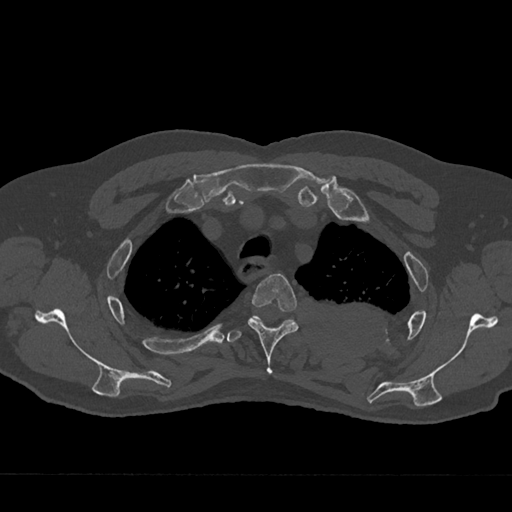
CT including the spine, one axial slice; position 559 of 797 along the scan axis; reconstruction kernel Br40s/3; 120 kVp; bone window (W 1800 / L 400 HU); 0.5 mm slice thickness; 512 × 512 image matrix, field of view 377 × 377 mm. Male patient, age 75 years. From the clinical record (not read from this slice): primary cancer: renal; vertebrae with lytic lesions (as recorded): T4.
Structures marked on this image (semi-automatic segmentation, software-assisted and operator-edited):
- T3 vertebra: bounding box [x1, y1, x2, y2] px = [248, 273, 299, 374]
- T4 vertebra: [227, 315, 295, 342]